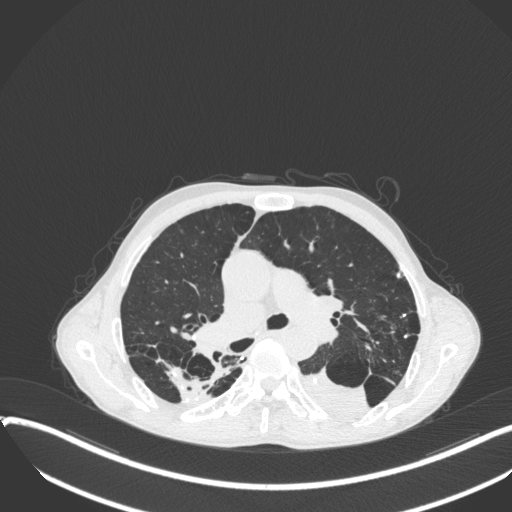
Chest CT, one axial slice; position 239 of 400 along the scan axis; 120 kVp; lung window (W 1500 / L -600 HU); 1 mm slice thickness; 512 × 512 image matrix, field of view 400 × 400 mm. Male patient, age 57 years. From the clinical record (not read from this slice): clinical TNM (as recorded): T4 N0 M0.
Outlined on this slice (bounding box drawn by a radiologist):
- lung tumour (recorded histology: squamous cell carcinoma): box from (x=296, y=366) to (x=372, y=421) px